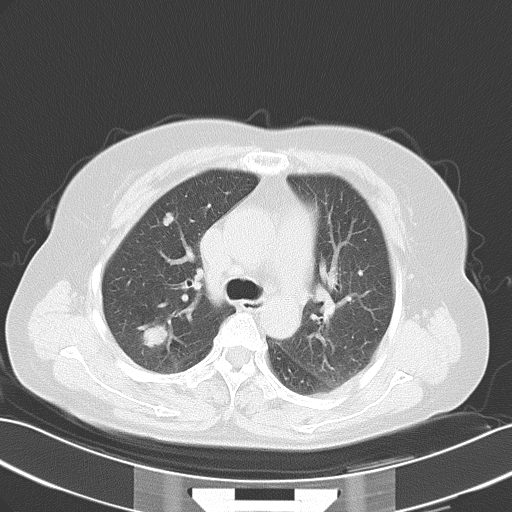
Chest CT, one axial slice; position 34 of 49 along the scan axis; reconstruction kernel B70f; lung window (W 1500 / L -600 HU); 5 mm slice thickness; 512 × 512 image matrix. Patient: female, 52 years. Case-level facts recorded for this patient, not image findings: clinical TNM (as recorded): T1c N3 M1a.
Structures marked on this image (bounding box drawn by a radiologist):
- lung tumour (recorded histology: adenocarcinoma): box from (x=132, y=316) to (x=175, y=352) px